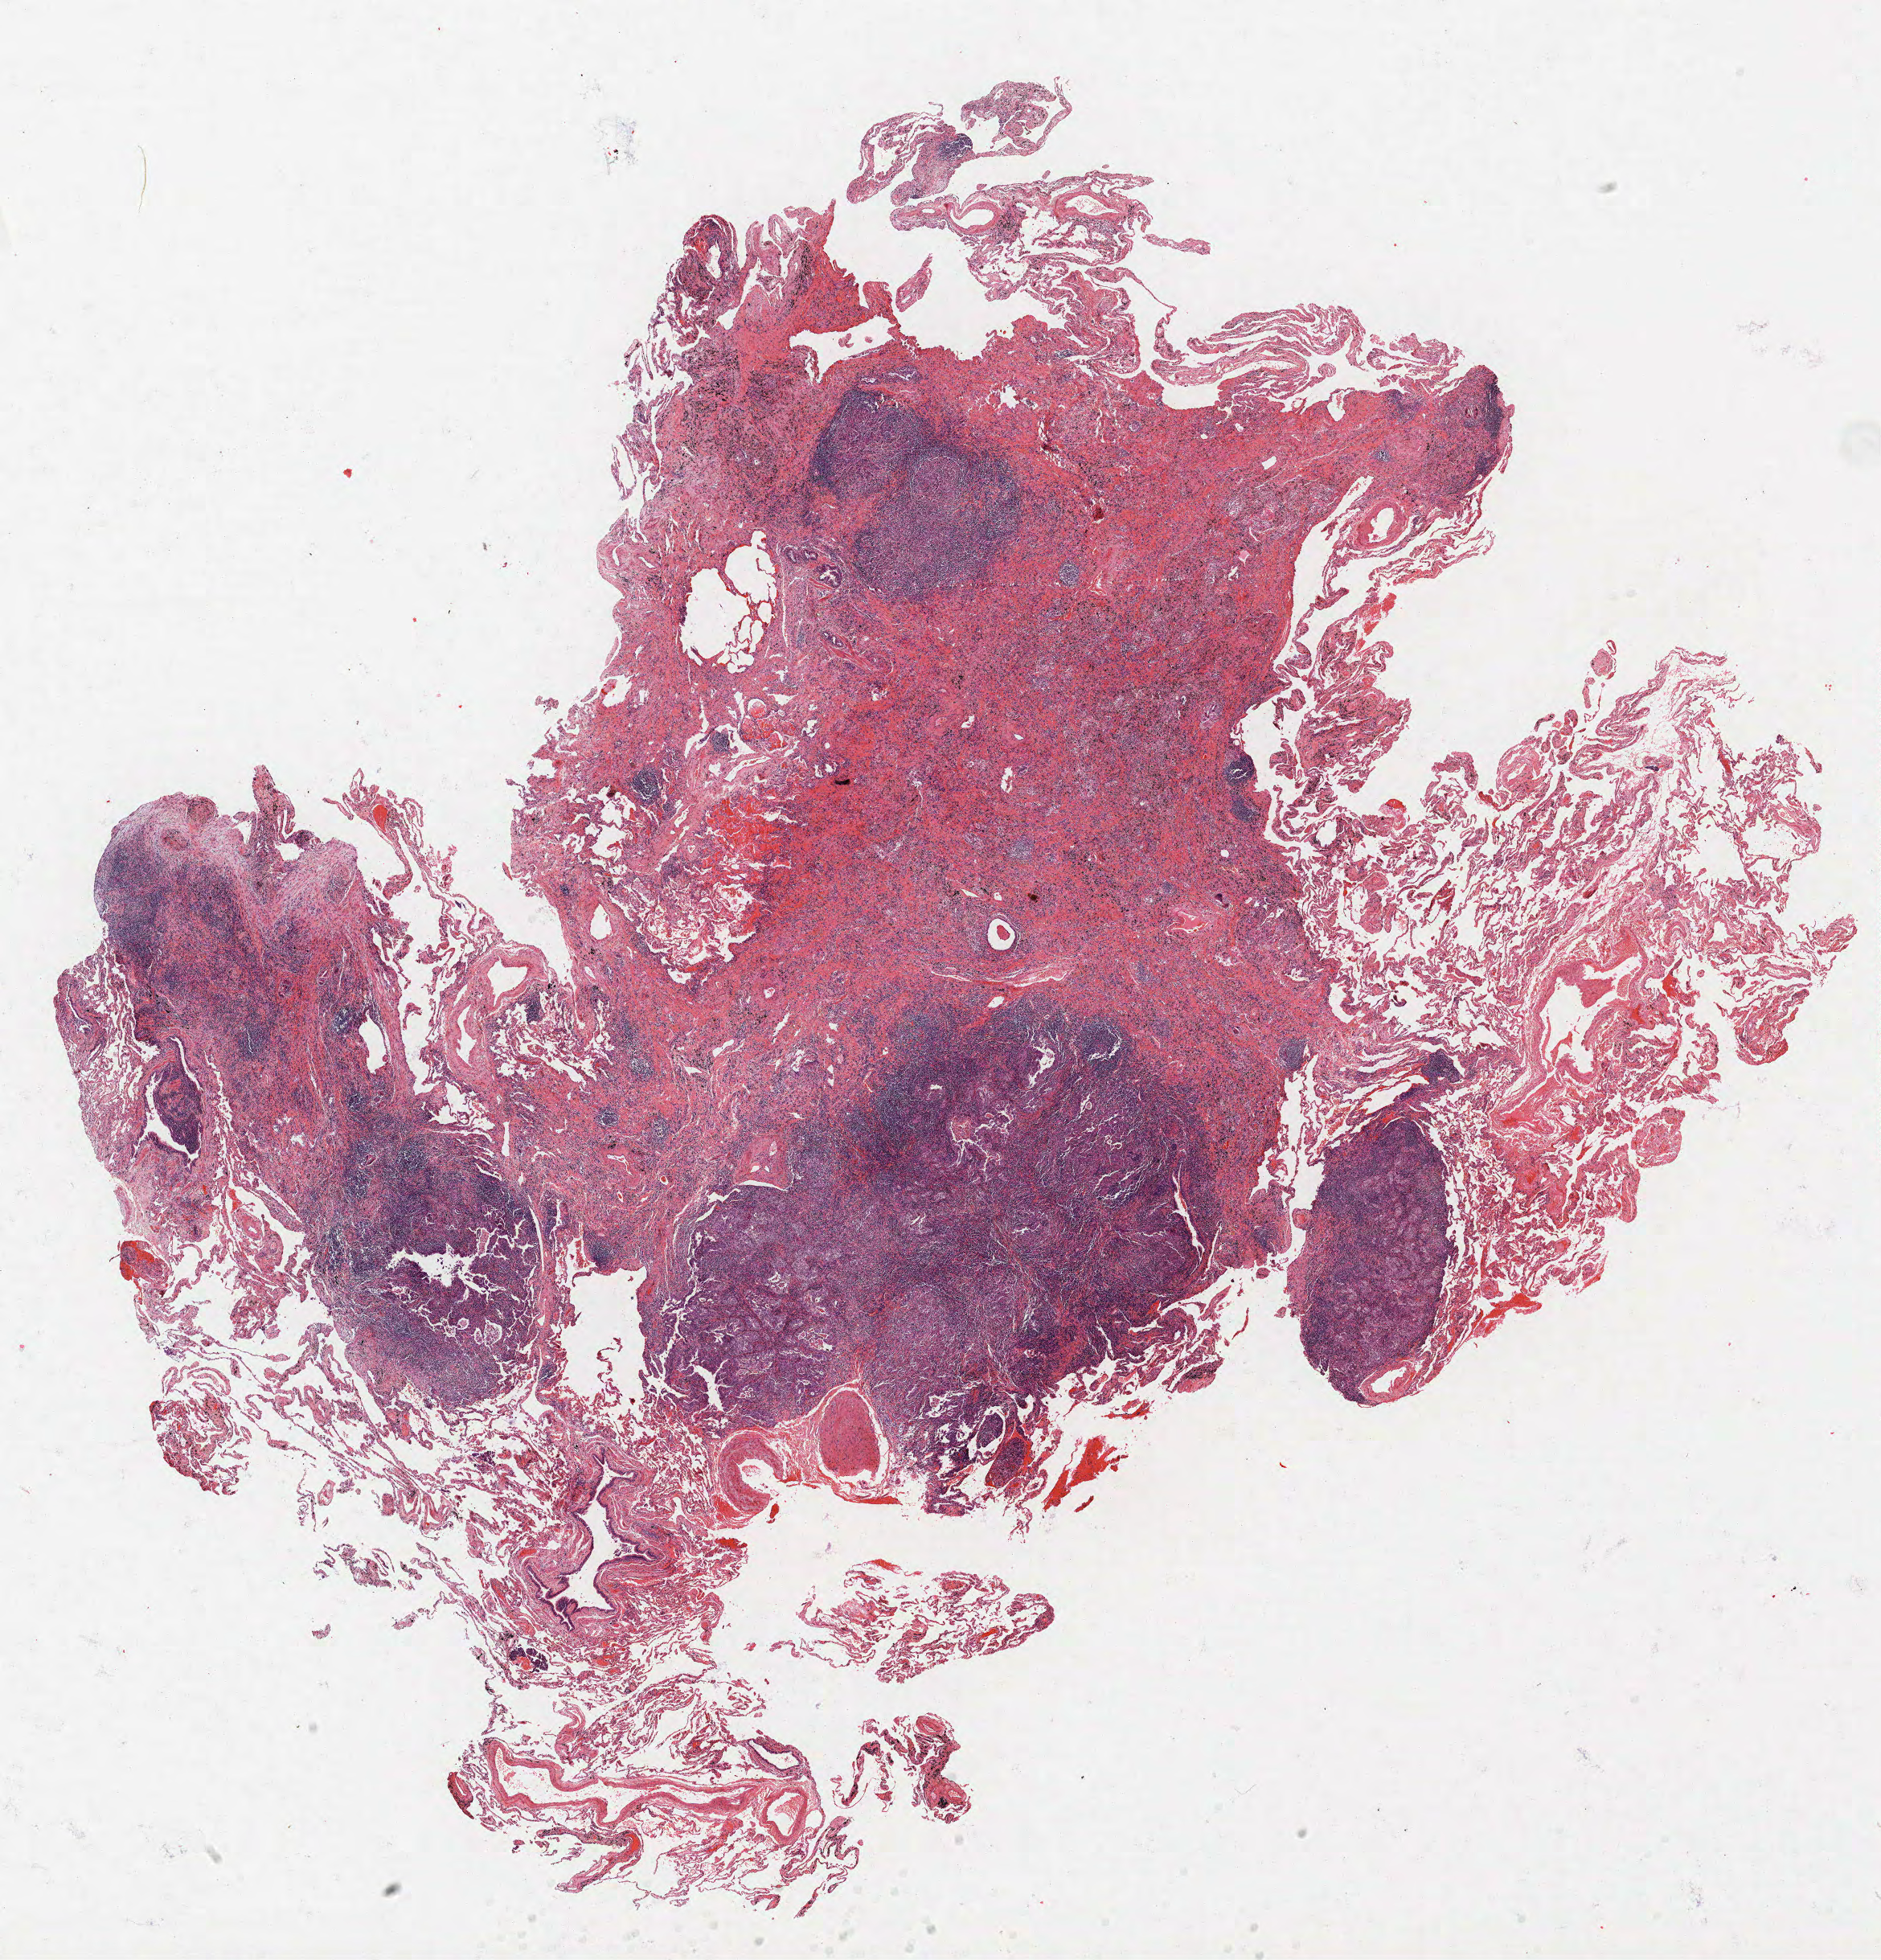
Whole-slide histology image, Hematoxylin and eosin (H&E) stained, low-resolution overview of the scanned area, about 18.7 x 19.5 mm (acquisition: 40x scan). FFPE section. Lung tissue. Male patient, aged 74 at enrolment. Former smoker at enrolment. Grade: poorly differentiated (G3).
Primary tumour location (clinical record): right upper lobe. Participant's lung-cancer diagnosis: Adenocarcinoma, NOS (ICD-O-3 8140/3). Tumour size (pathology): 6 mm. Stage (AJCC 6th edition): IA.